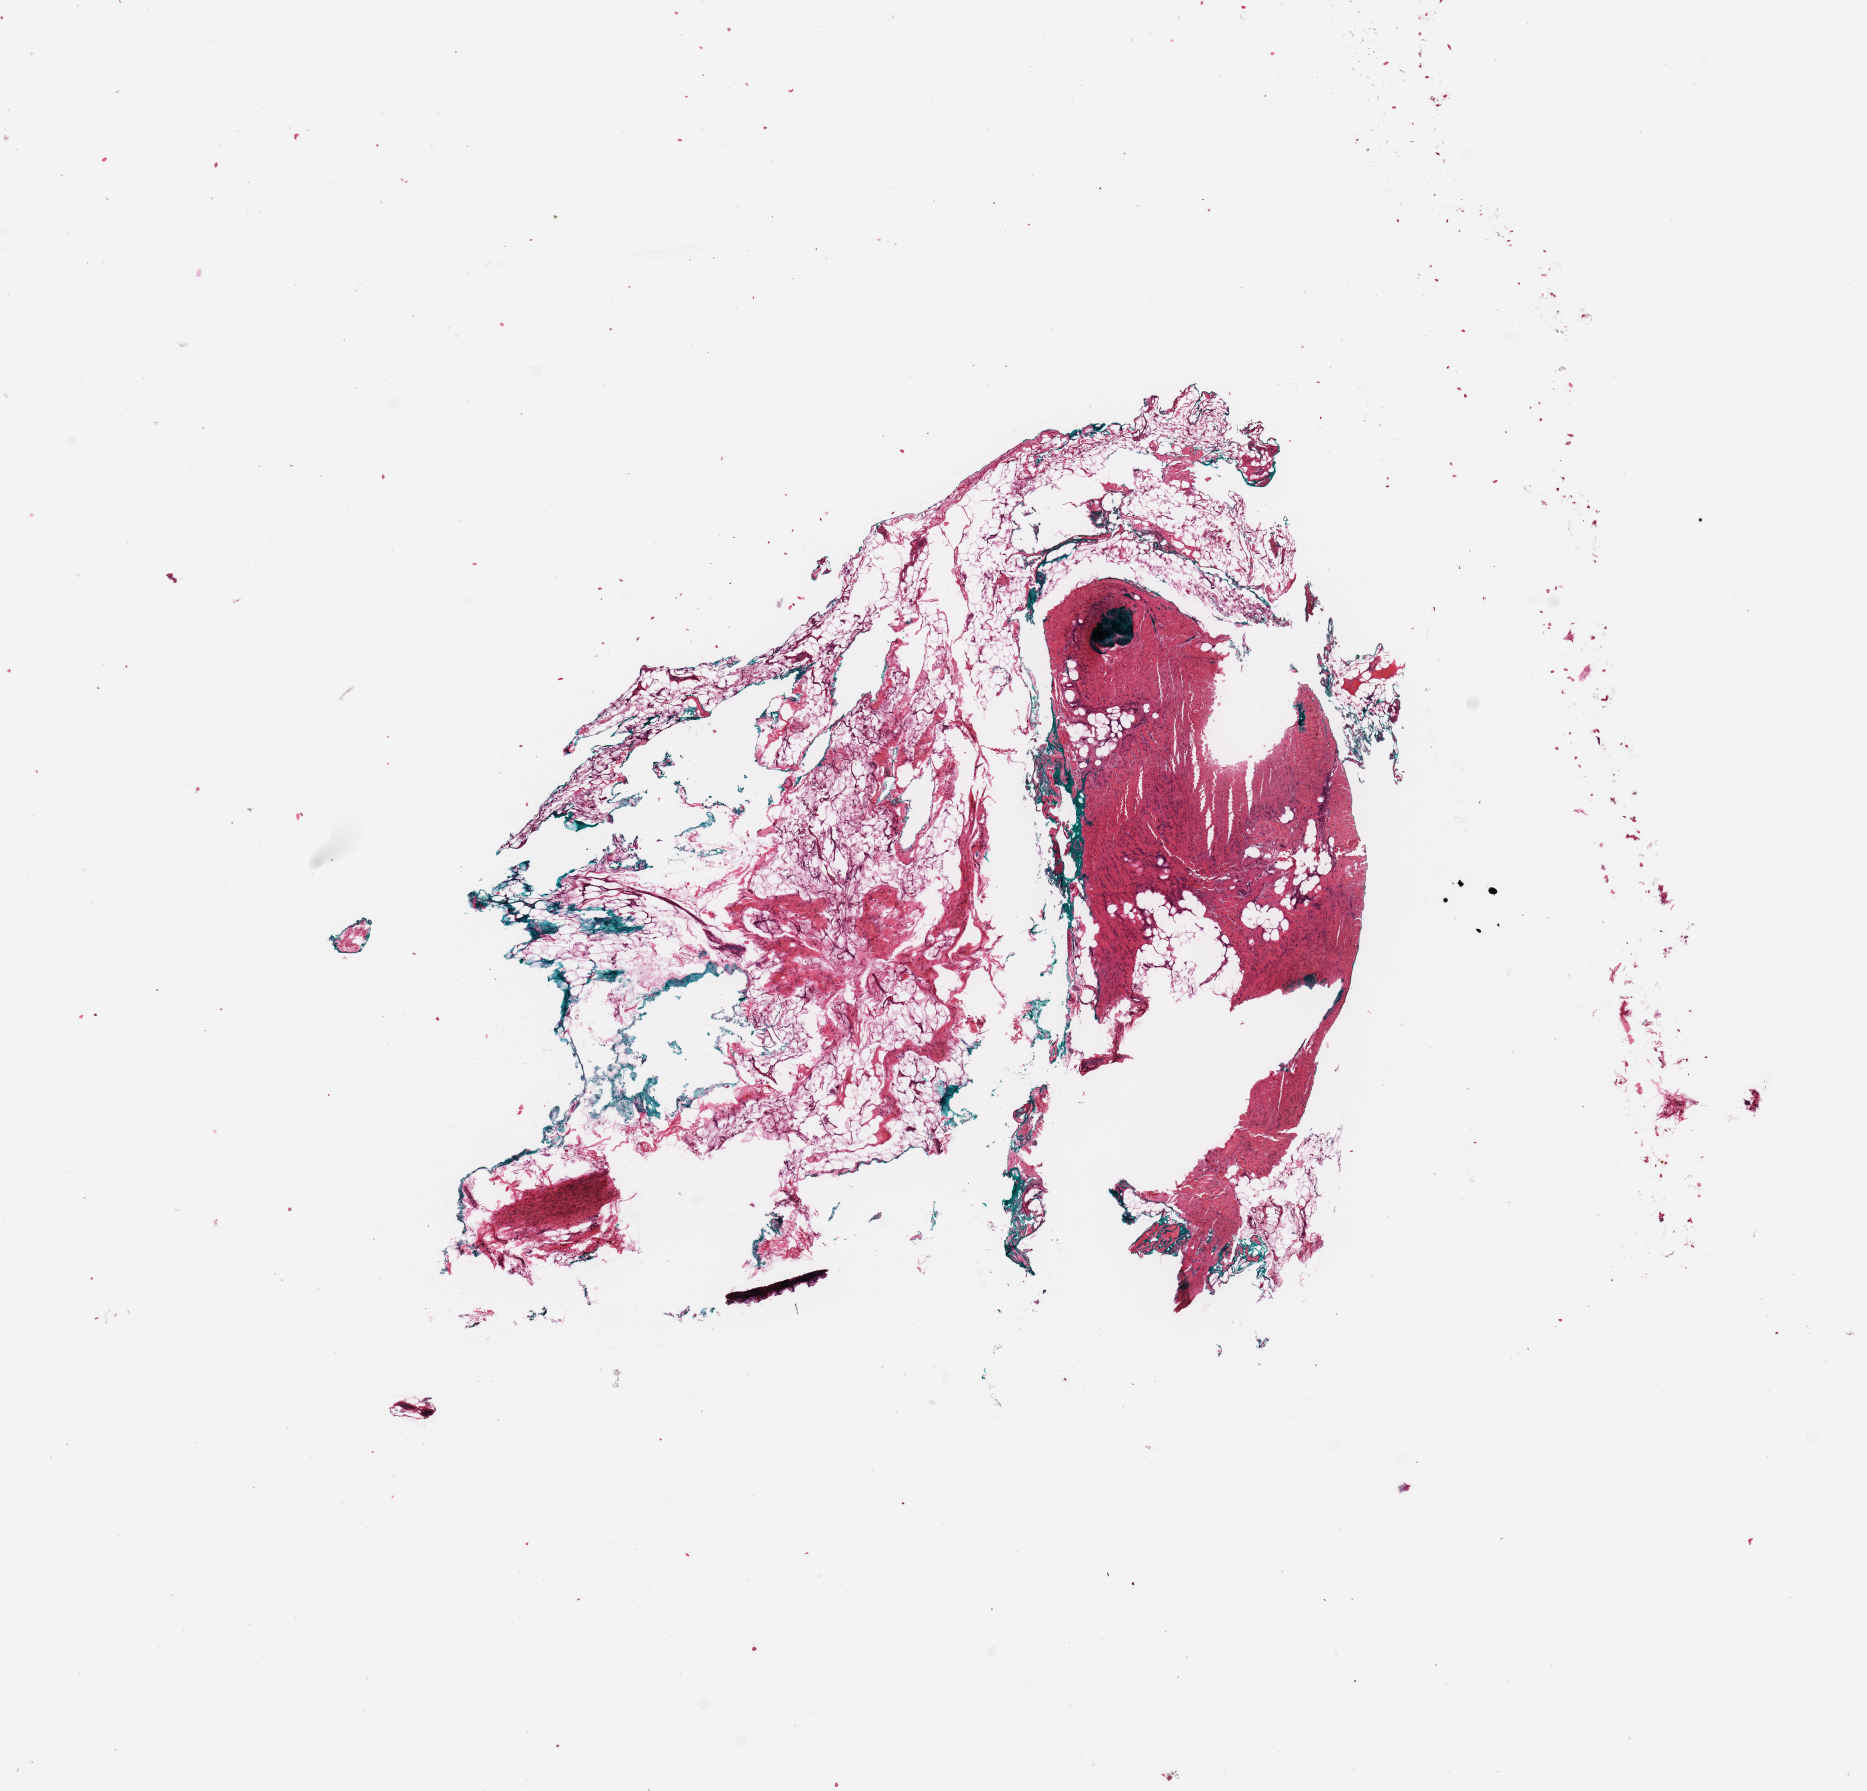
Digitized Hematoxylin and eosin (H&E) stained tissue section (whole slide), a low-resolution overview of the entire scanned area, about 14.8 x 14.2 mm (slide scanned at 20x), normal (non-tumour) tissue sample. 62-year-old female patient.
This section: normal (non-tumour) tissue from the same patient. Patient diagnosis (cohort enrolment): sarcoma (site not recorded at cohort level).